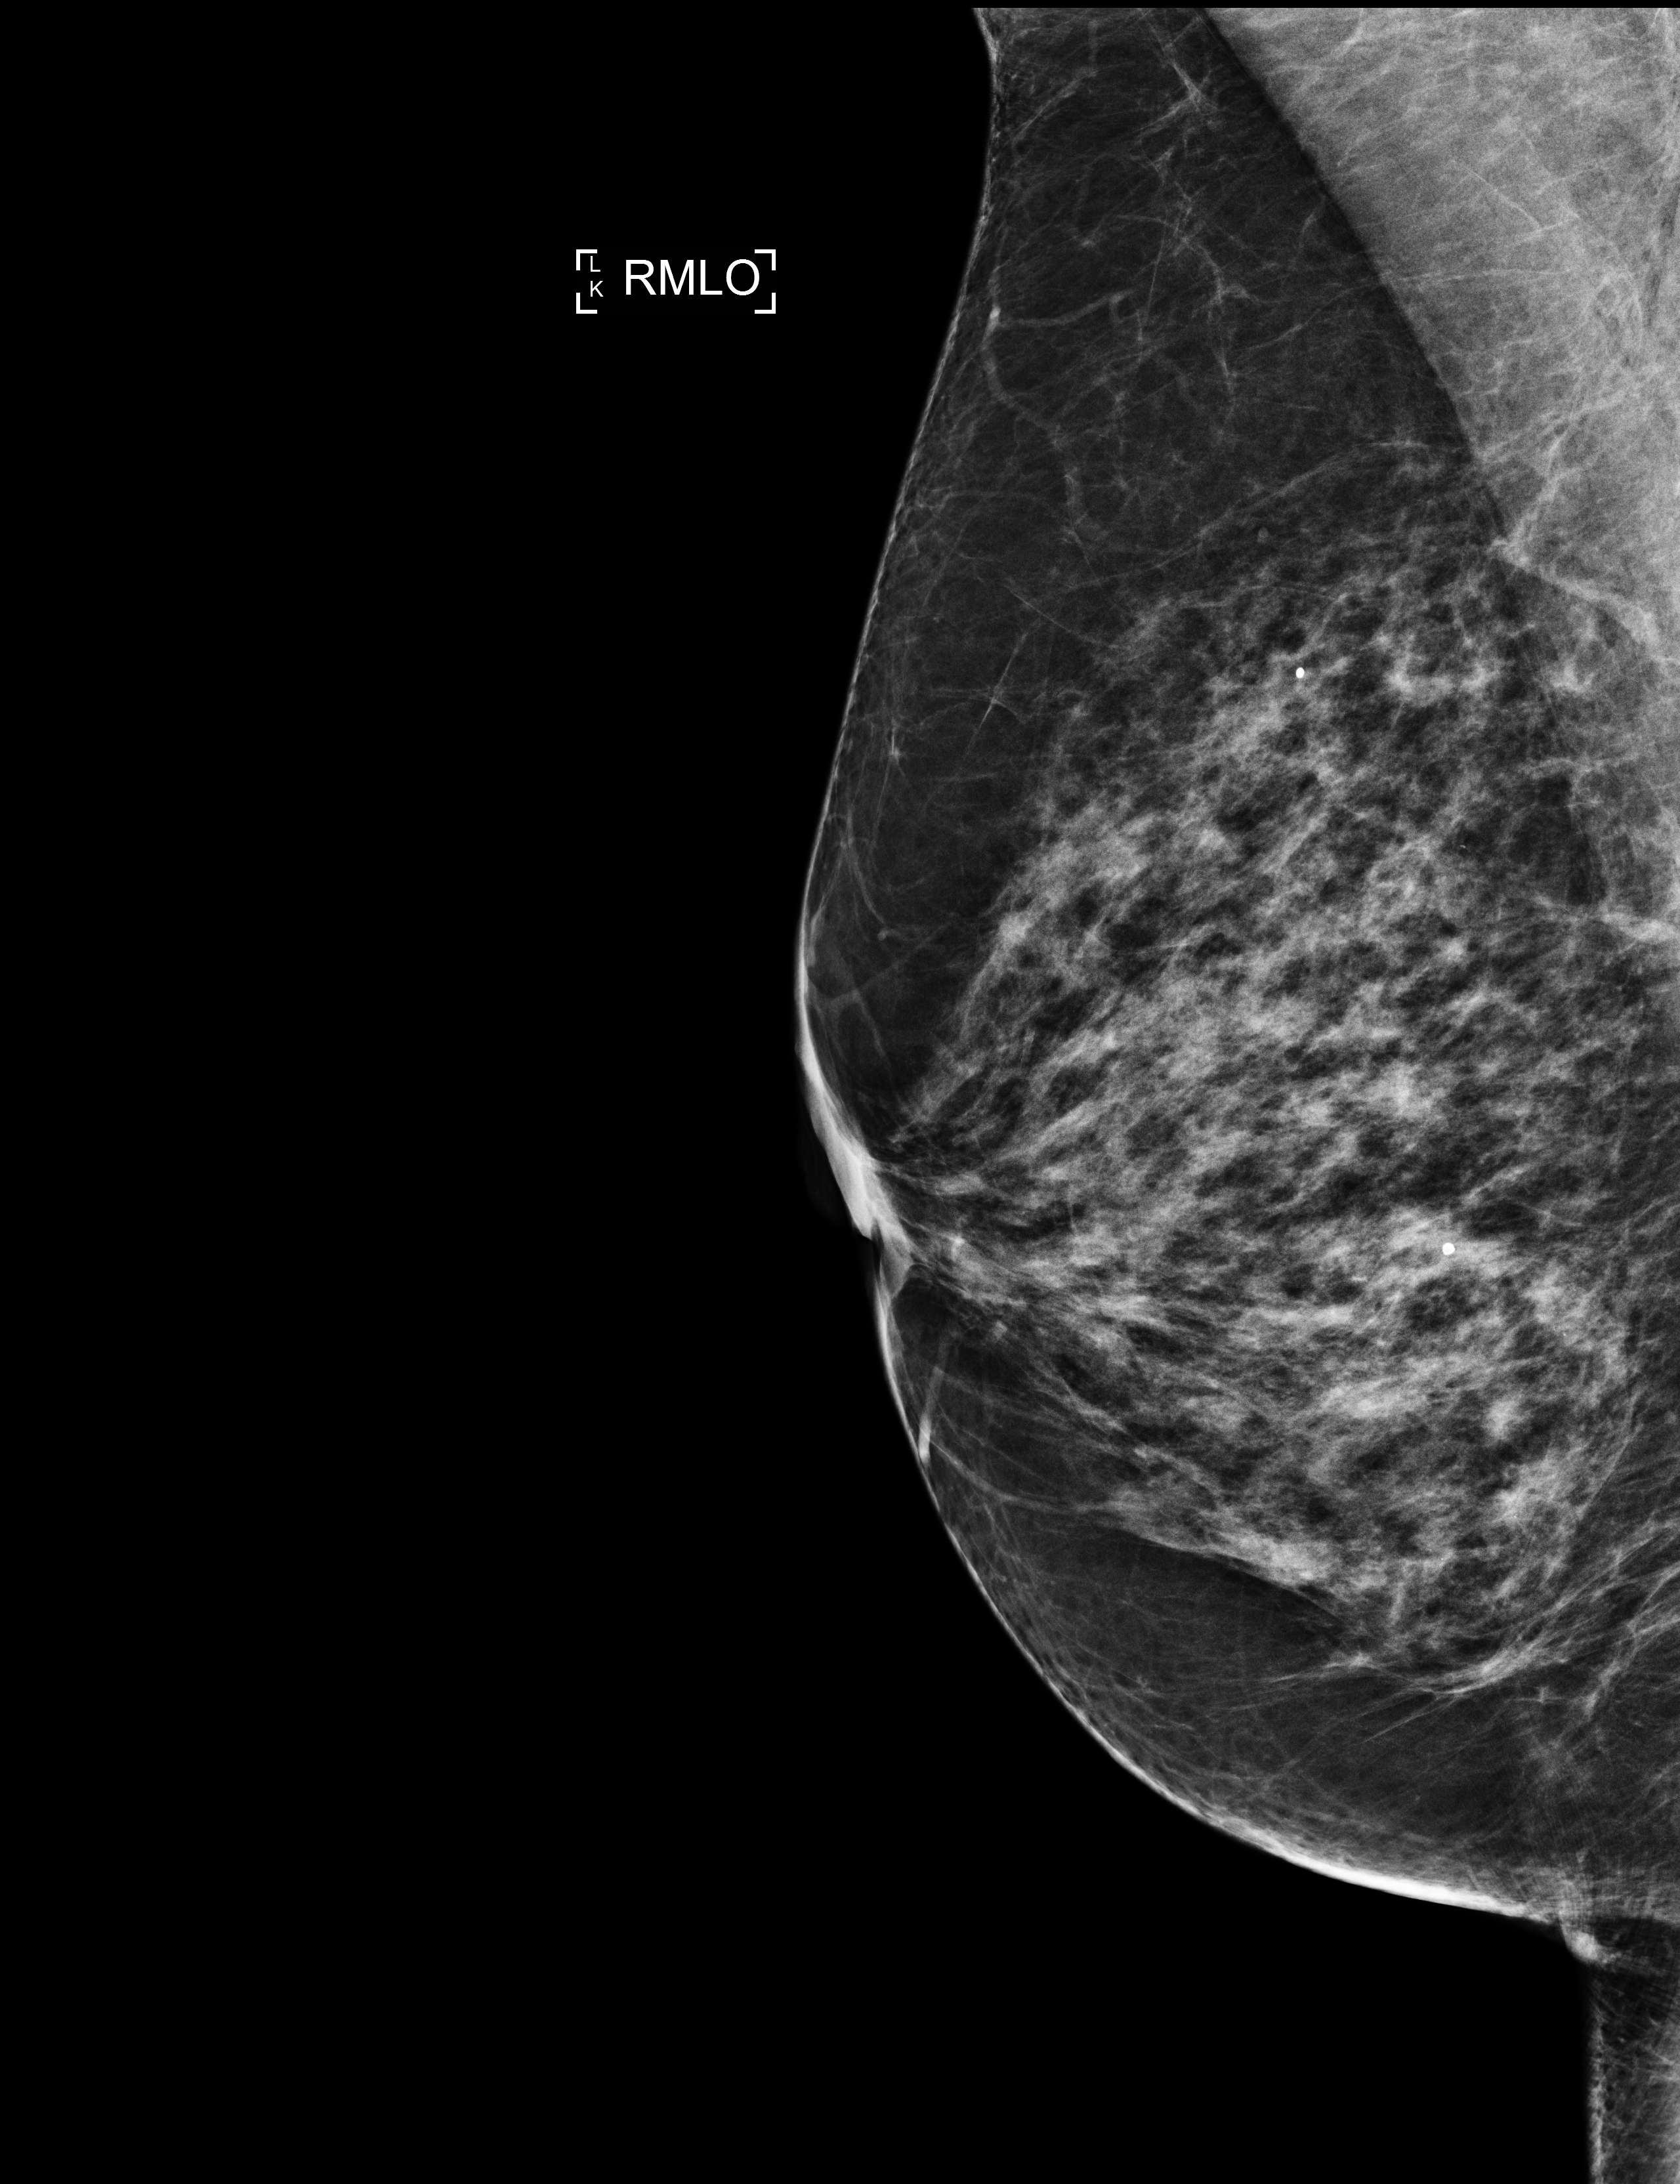
Screening examination; compressed breast thickness 61 mm; system: Selenia Dimensions. Patient: female, 61 years.
Image type: full-field digital mammogram. Breast: right. Projection: mediolateral oblique (MLO) view.